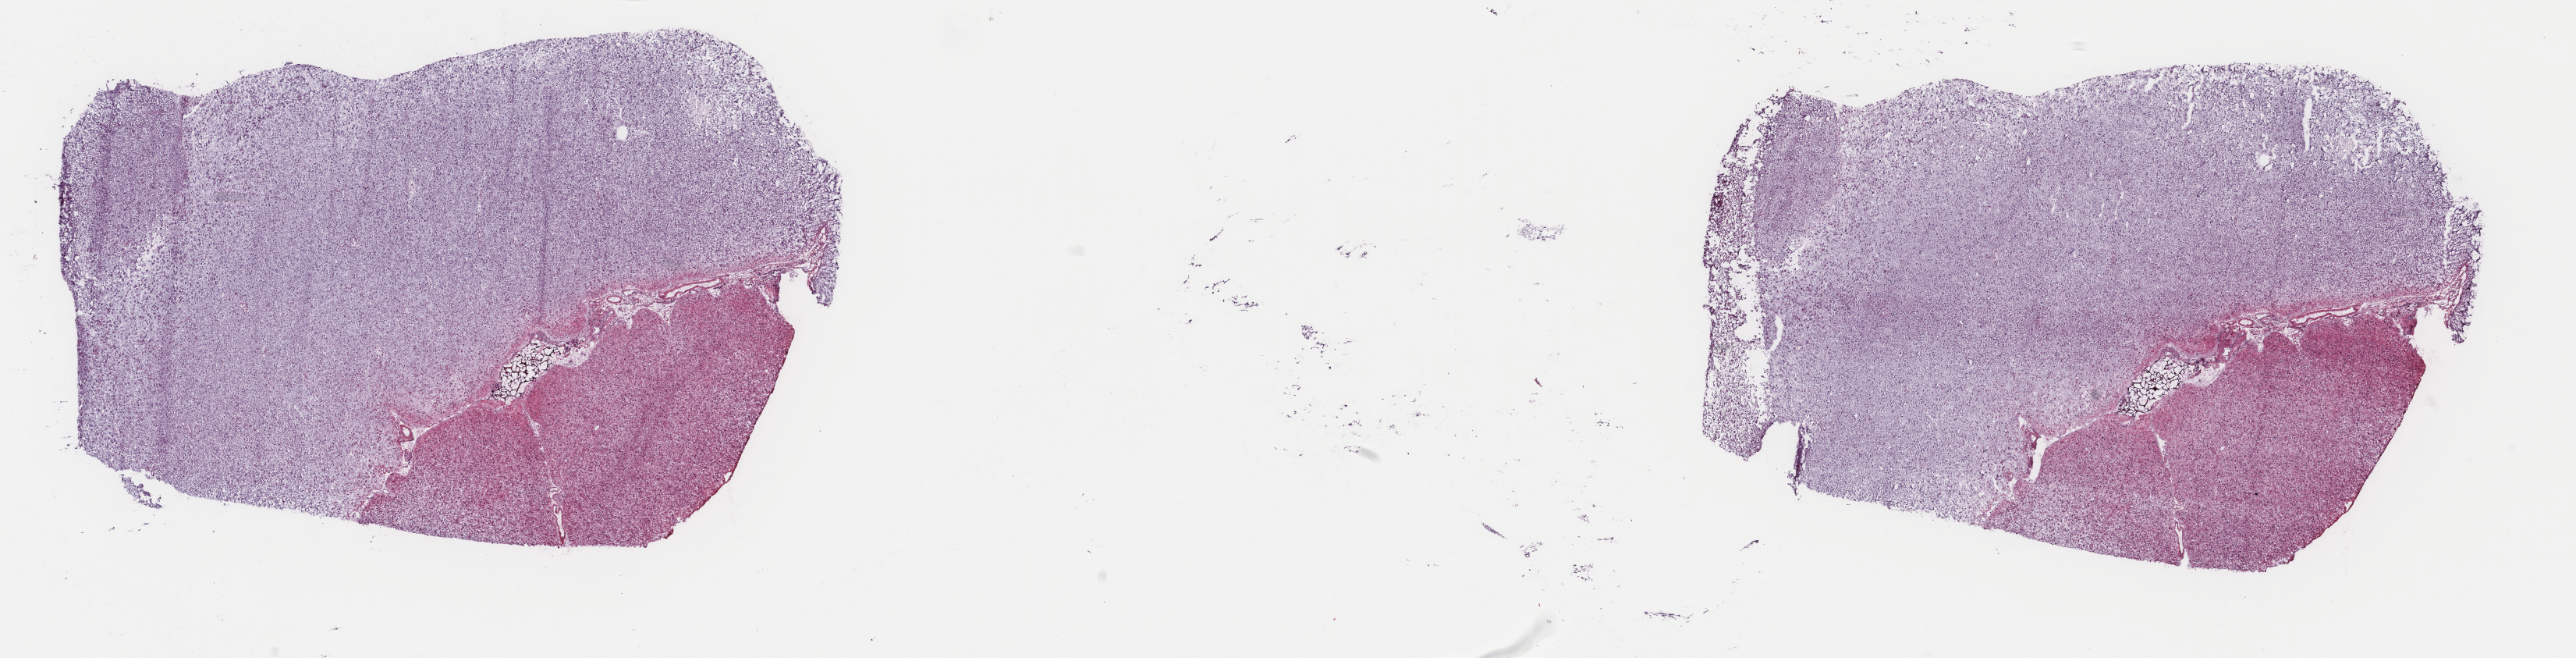
Digitized H&E-stained tissue section (whole slide) — a low-resolution overview of the entire scanned area, about 26.2 x 6.7 mm (slide scanned at 40x); frozen section; sample: primary tumour, brain. Patient: female, age at initial diagnosis 49 years.
Pathologic diagnosis: Oligodendroglioma, anaplastic (cerebrum).